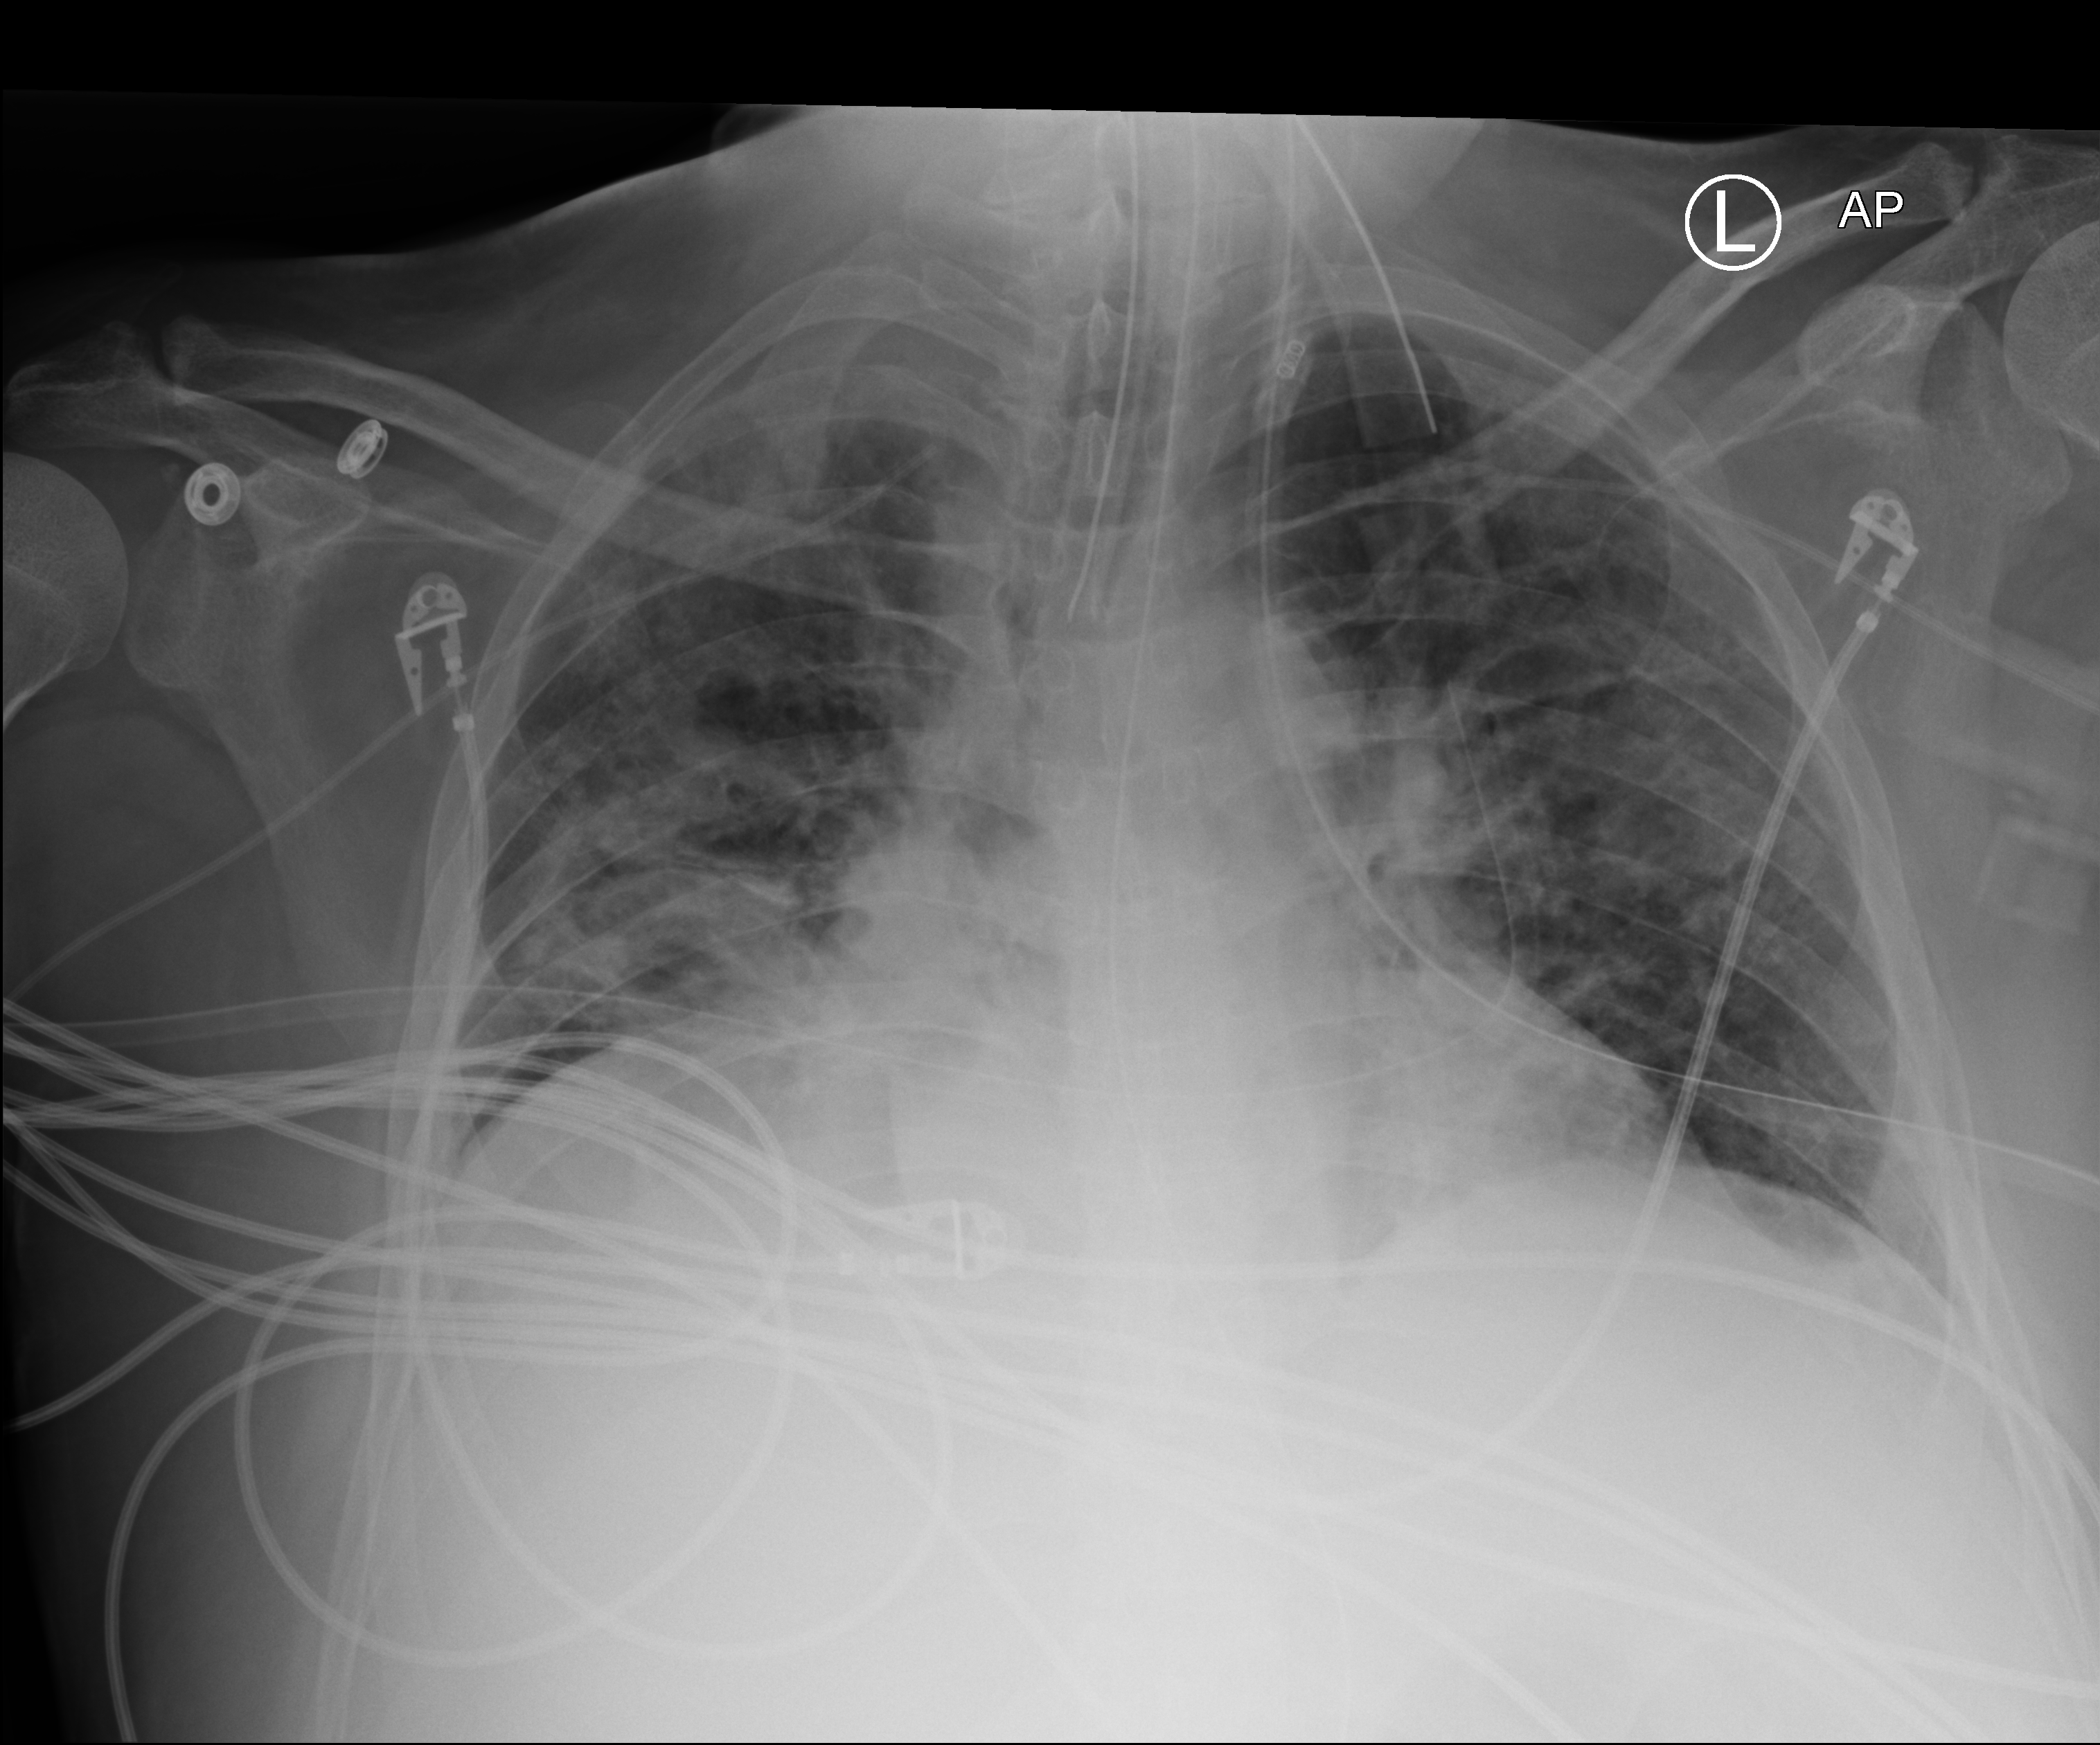
Bedside chest radiograph (computed radiography). Adult patient hospitalised with COVID-19, age 18–59 years.
From the hospital-stay record, not from the radiograph (when in the stay this image was taken is not recorded): length of hospital stay: 50 days; mechanically ventilated during this hospital stay: yes; admitted to intensive care during this hospital stay: yes.